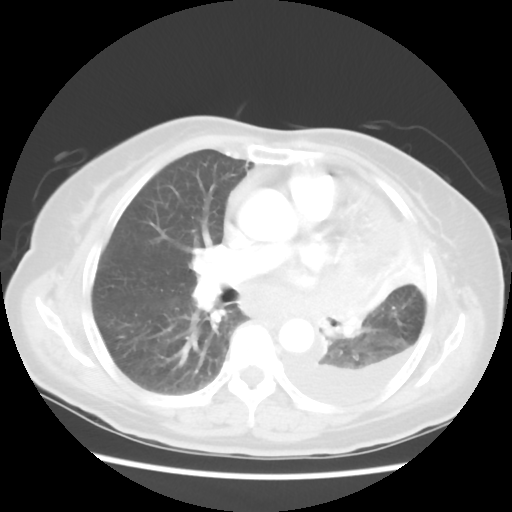
Chest CT, one axial slice; position 30 of 52 along the scan axis; lung window (W 1500 / L -600 HU); 5 mm slice thickness; 512 × 512 image matrix. Female patient, age 72 years. From the clinical record (not read from this slice): clinical TNM (as recorded): T4 N3 M1b; histopathological grade: G3.
Outlined on this slice (rectangle marked by the reading radiologist):
- lung tumour (recorded histology: large cell carcinoma): bounding box [x1, y1, x2, y2] px = [310, 262, 381, 347]